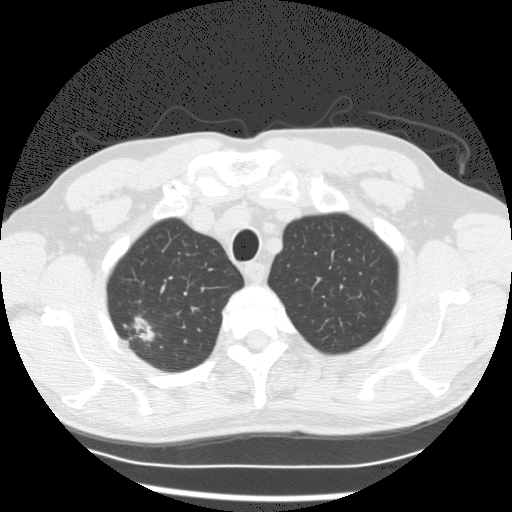
Axial slice from a low-dose chest CT screening exam; first (baseline) screen; lung window (W 1500 / L -600 HU); 2.5 mm slice thickness; standard (soft-tissue) reconstruction kernel (STANDARD); 512 × 512 image matrix, field of view 351 × 351 mm. Male participant, aged 63 years at enrolment.
- Expert reader's lesion annotation, bounding box <107,300,174,363> (left, top, right, bottom; pixels).
- Reader record for this screening exam (exam-level; its link to the box is not recorded): non-calcified nodule or mass ≥4 mm, right upper lobe, 19 × 9 mm, poorly defined margins, mixed attenuation.
- Participant outcome: lung cancer diagnosed 152 days after this screen — bronchiolo-alveolar adenocarcinoma, NOS, right upper lobe, moderately differentiated (G2), stage IA (AJCC 6th edition), 15 mm at pathology.